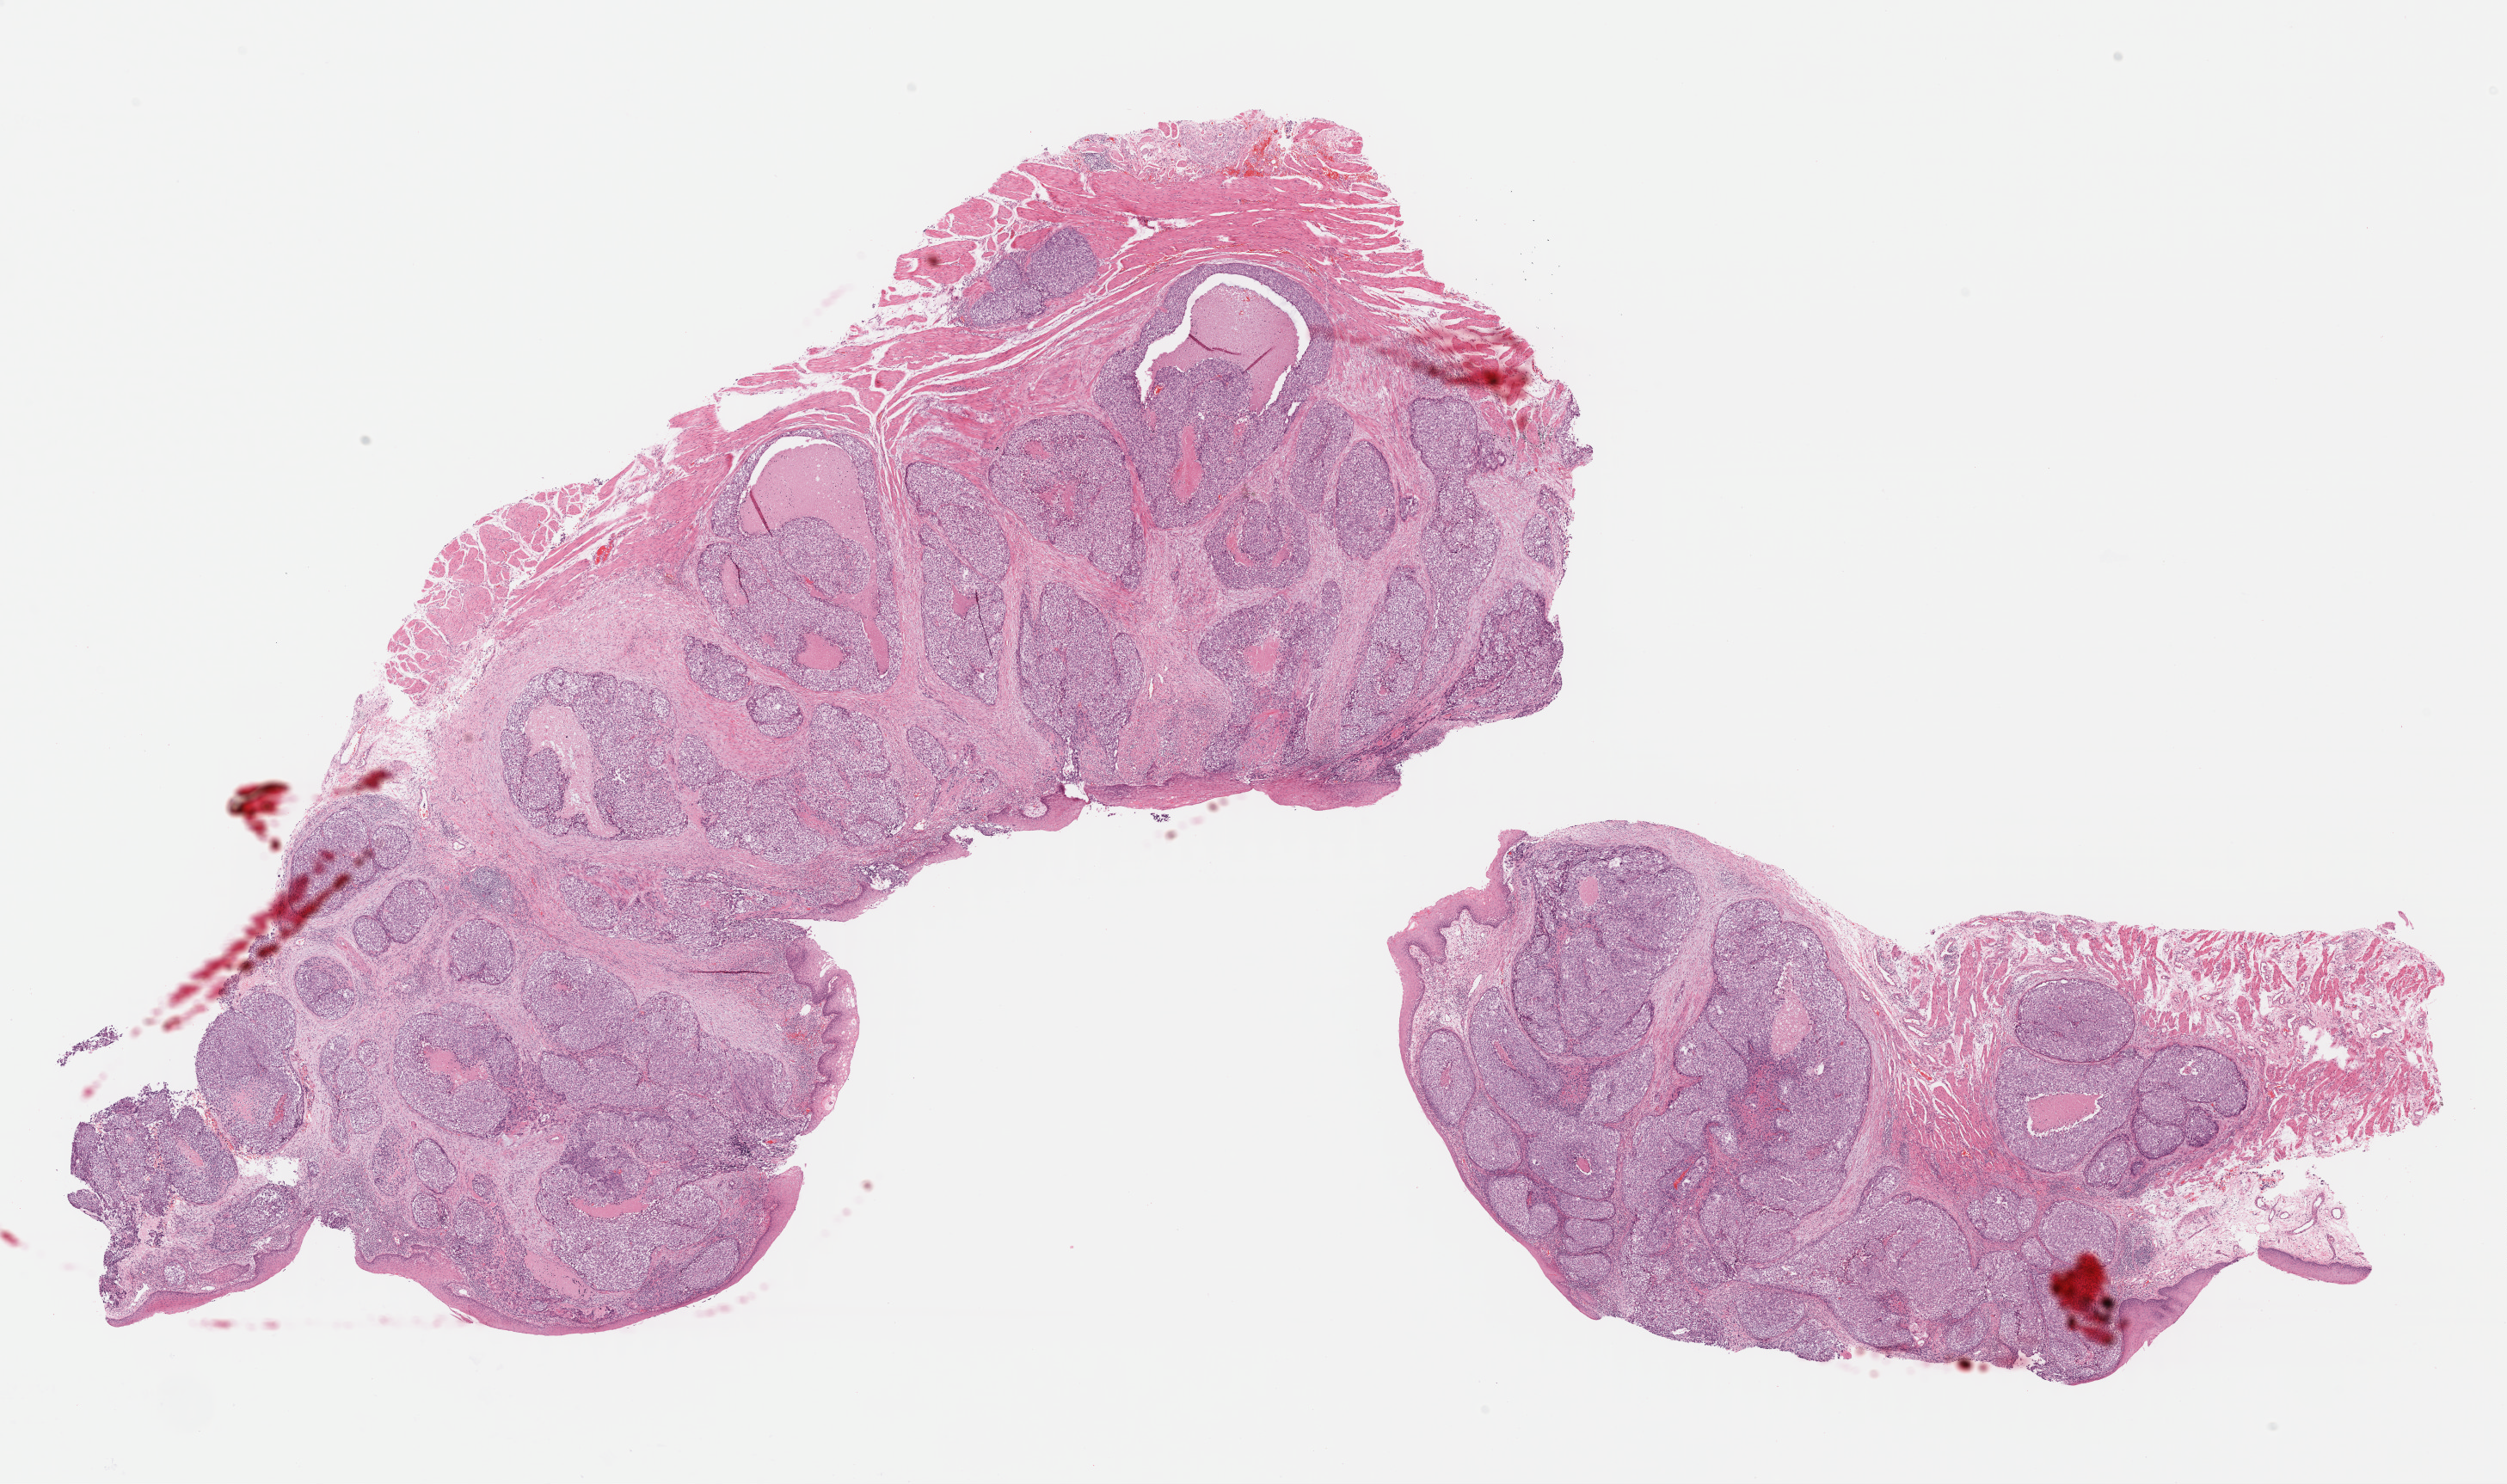
H&E whole-slide image, a low-resolution overview of the entire scanned area, about 22.9 x 13.6 mm, FFPE section, esophagus, primary tumour sample. Female, age 69 years at initial diagnosis. Histologic grade: G2 (moderately differentiated).
• lymph nodes positive (case pathology): 0 of 2 examined
• pathologic diagnosis: Squamous cell carcinoma, NOS
• TNM: T3 N0 M0
• AJCC pathologic stage: IIB